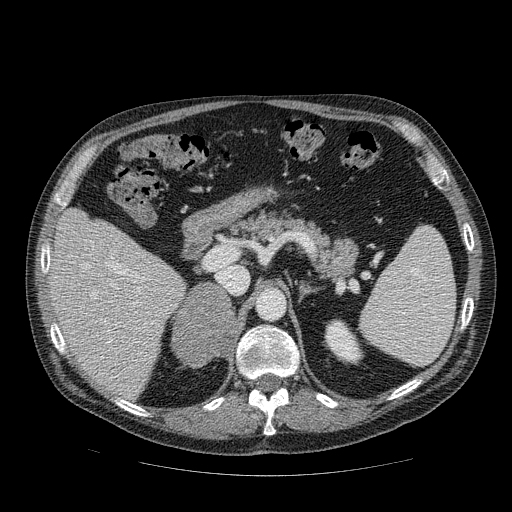
Contrast-enhanced abdominal CT, one axial slice; slice 57 of 111 in the series (ordered by position); reconstruction kernel STANDARD; 120 kVp; intravenous contrast given; soft-tissue window (W 400 / L 40 HU); 2.5 mm slice thickness; 512 × 512 image matrix, field of view 420 × 420 mm. Patient: male, 56 years. Case-level facts recorded for this patient, not image findings: diagnosis: adrenocortical carcinoma; tumour side: right adrenal; tumour size at pathology: 9 cm; Ki-67 index: 48 %; stage (as recorded): 4.
Annotated regions visible in this slice (semi-automatic segmentation, software-assisted and operator-edited):
- mass: bounding box <172,284,237,365> (left, top, right, bottom; pixels)